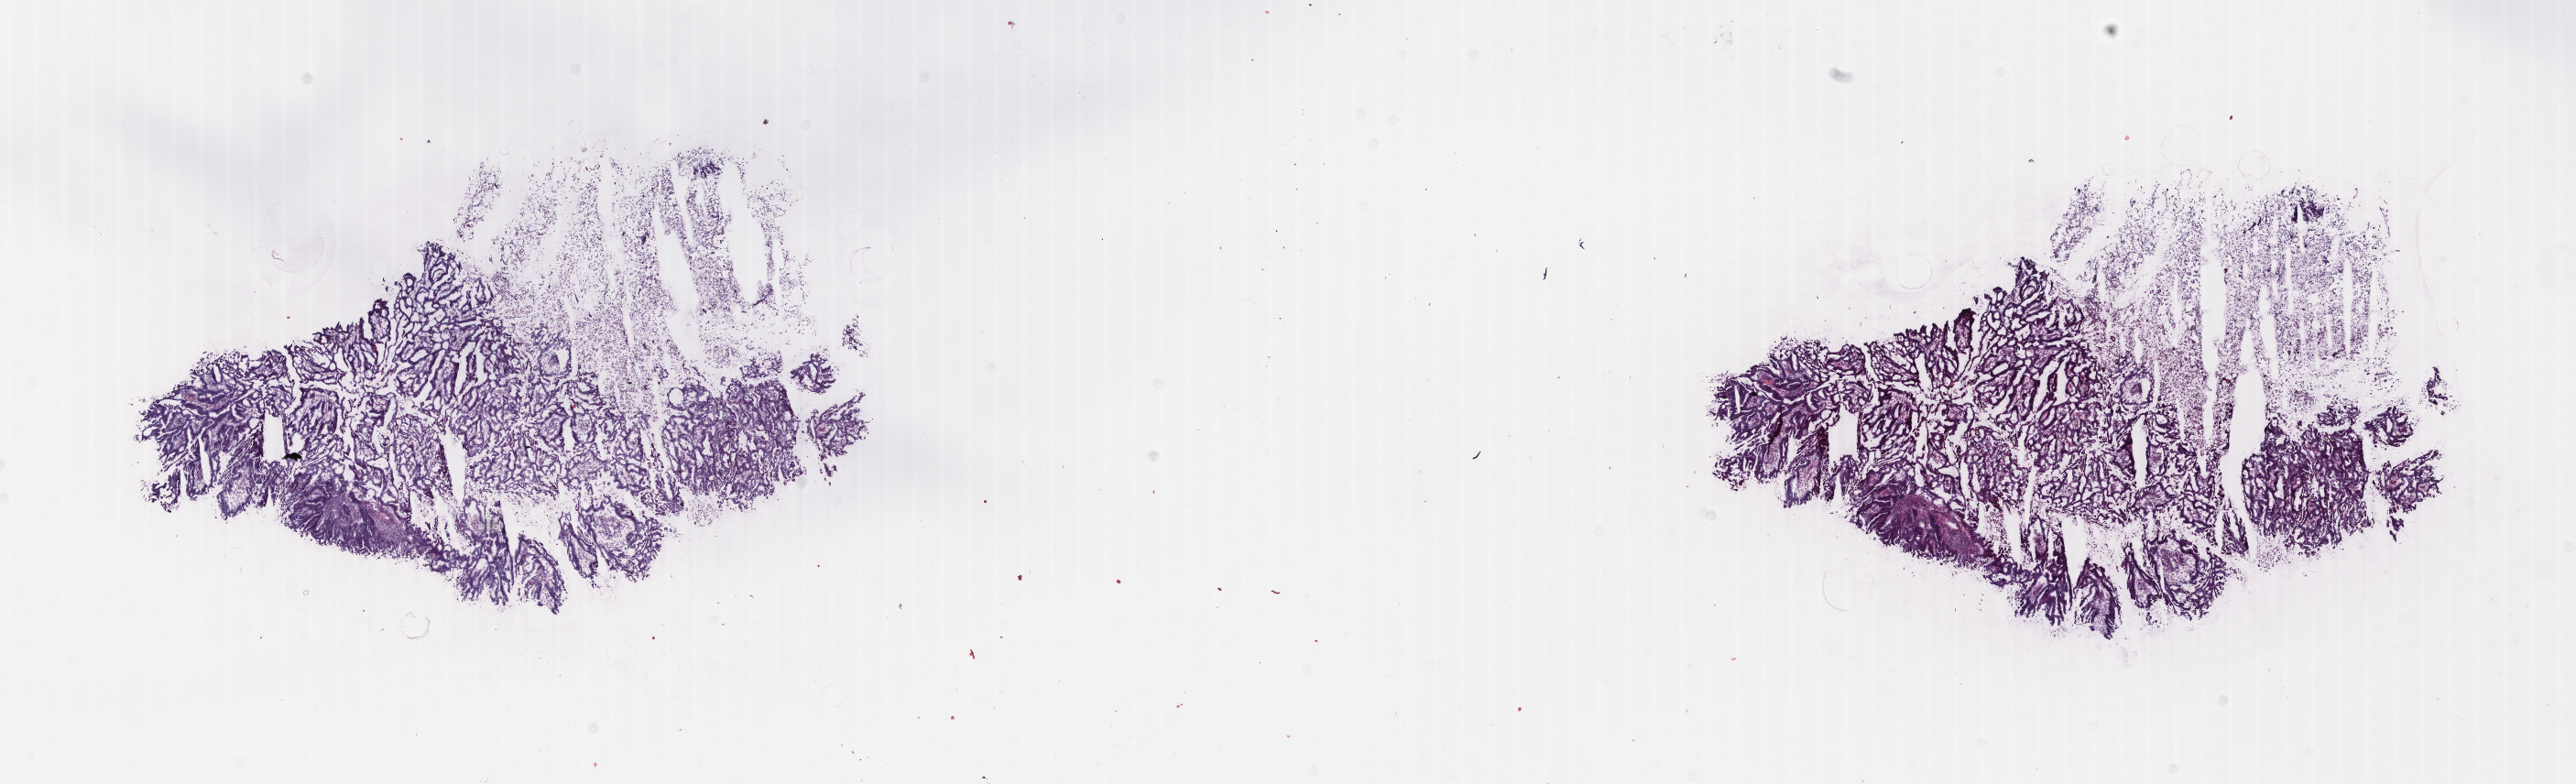
Digitized Hematoxylin and eosin (H&E) stained tissue section (whole slide) — shown as a low-resolution overview of the whole scanned area (about 22.4 x 6.8 mm), frozen section, primary tumour sample from the uterus. Female patient; age at initial diagnosis 61 years. Histologic grade: G2 (moderately differentiated). Composition of this section per pathologist review: tumour cells 78%, tumour nuclei 80%, normal cells 0%, stromal cells 20%, necrosis 2%. Infiltration values recorded for this section: lymphocyte infiltration 2%, monocyte infiltration 3%, neutrophil infiltration 8%.
FIGO stage: IC. Histologic diagnosis: Endometrioid adenocarcinoma, NOS (endometrium).